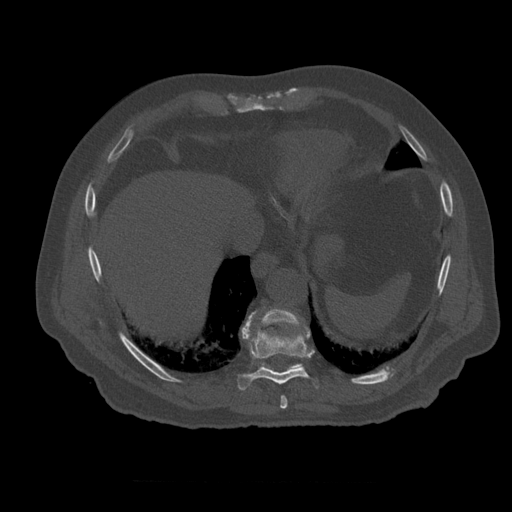
CT including the spine, one axial slice. Slice 318 of 399 in the series (ordered by position). Reconstruction kernel STANDARD. 120 kVp. Bone window (W 1800 / L 400 HU). 1.25 mm slice thickness. 512 × 512 image matrix, field of view 407 × 407 mm. Patient age 73 years. From the clinical record (not read from this slice): primary cancer: prostate.
Annotated regions visible in this slice (semi-automatically segmented with operator editing):
- T10 vertebra: box from (x=258, y=310) to (x=303, y=369) px
- T8 vertebra: (x=281, y=396)–(x=288, y=409)
- T9 vertebra: (x=238, y=312)–(x=311, y=391)